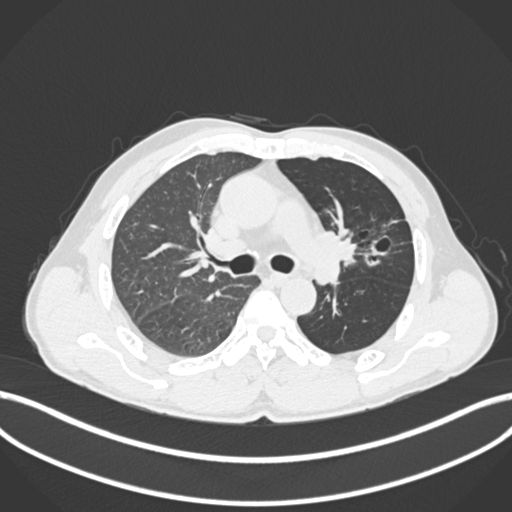
Chest CT, one axial slice; 120 kVp; lung window (W 1500 / L -600 HU); 1 mm slice thickness; 512 × 512 image matrix. Patient: male, 57 years. From the clinical record (not read from this slice): clinical TNM (as recorded): T2b N0 M0.
Annotated regions visible in this slice (rectangle marked by the reading radiologist):
- lung tumour (recorded histology: squamous cell carcinoma): bounding box (x1, y1, x2, y2) in pixels: (319, 224, 371, 267)